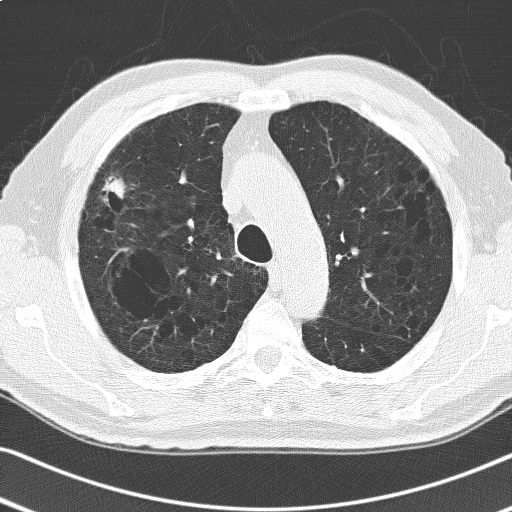
Low-dose screening chest CT, one axial slice. Slice 128 of 168 in the series (ordered by position). 120 kVp. Lung window (W 1500 / L -600 HU). 512 × 512 image matrix, field of view 336 × 336 mm.
Annotated regions visible in this slice (manually delineated by an expert):
- lesion 1 (tumor, upper lobe of right lung): box from (x=103, y=176) to (x=126, y=198) px